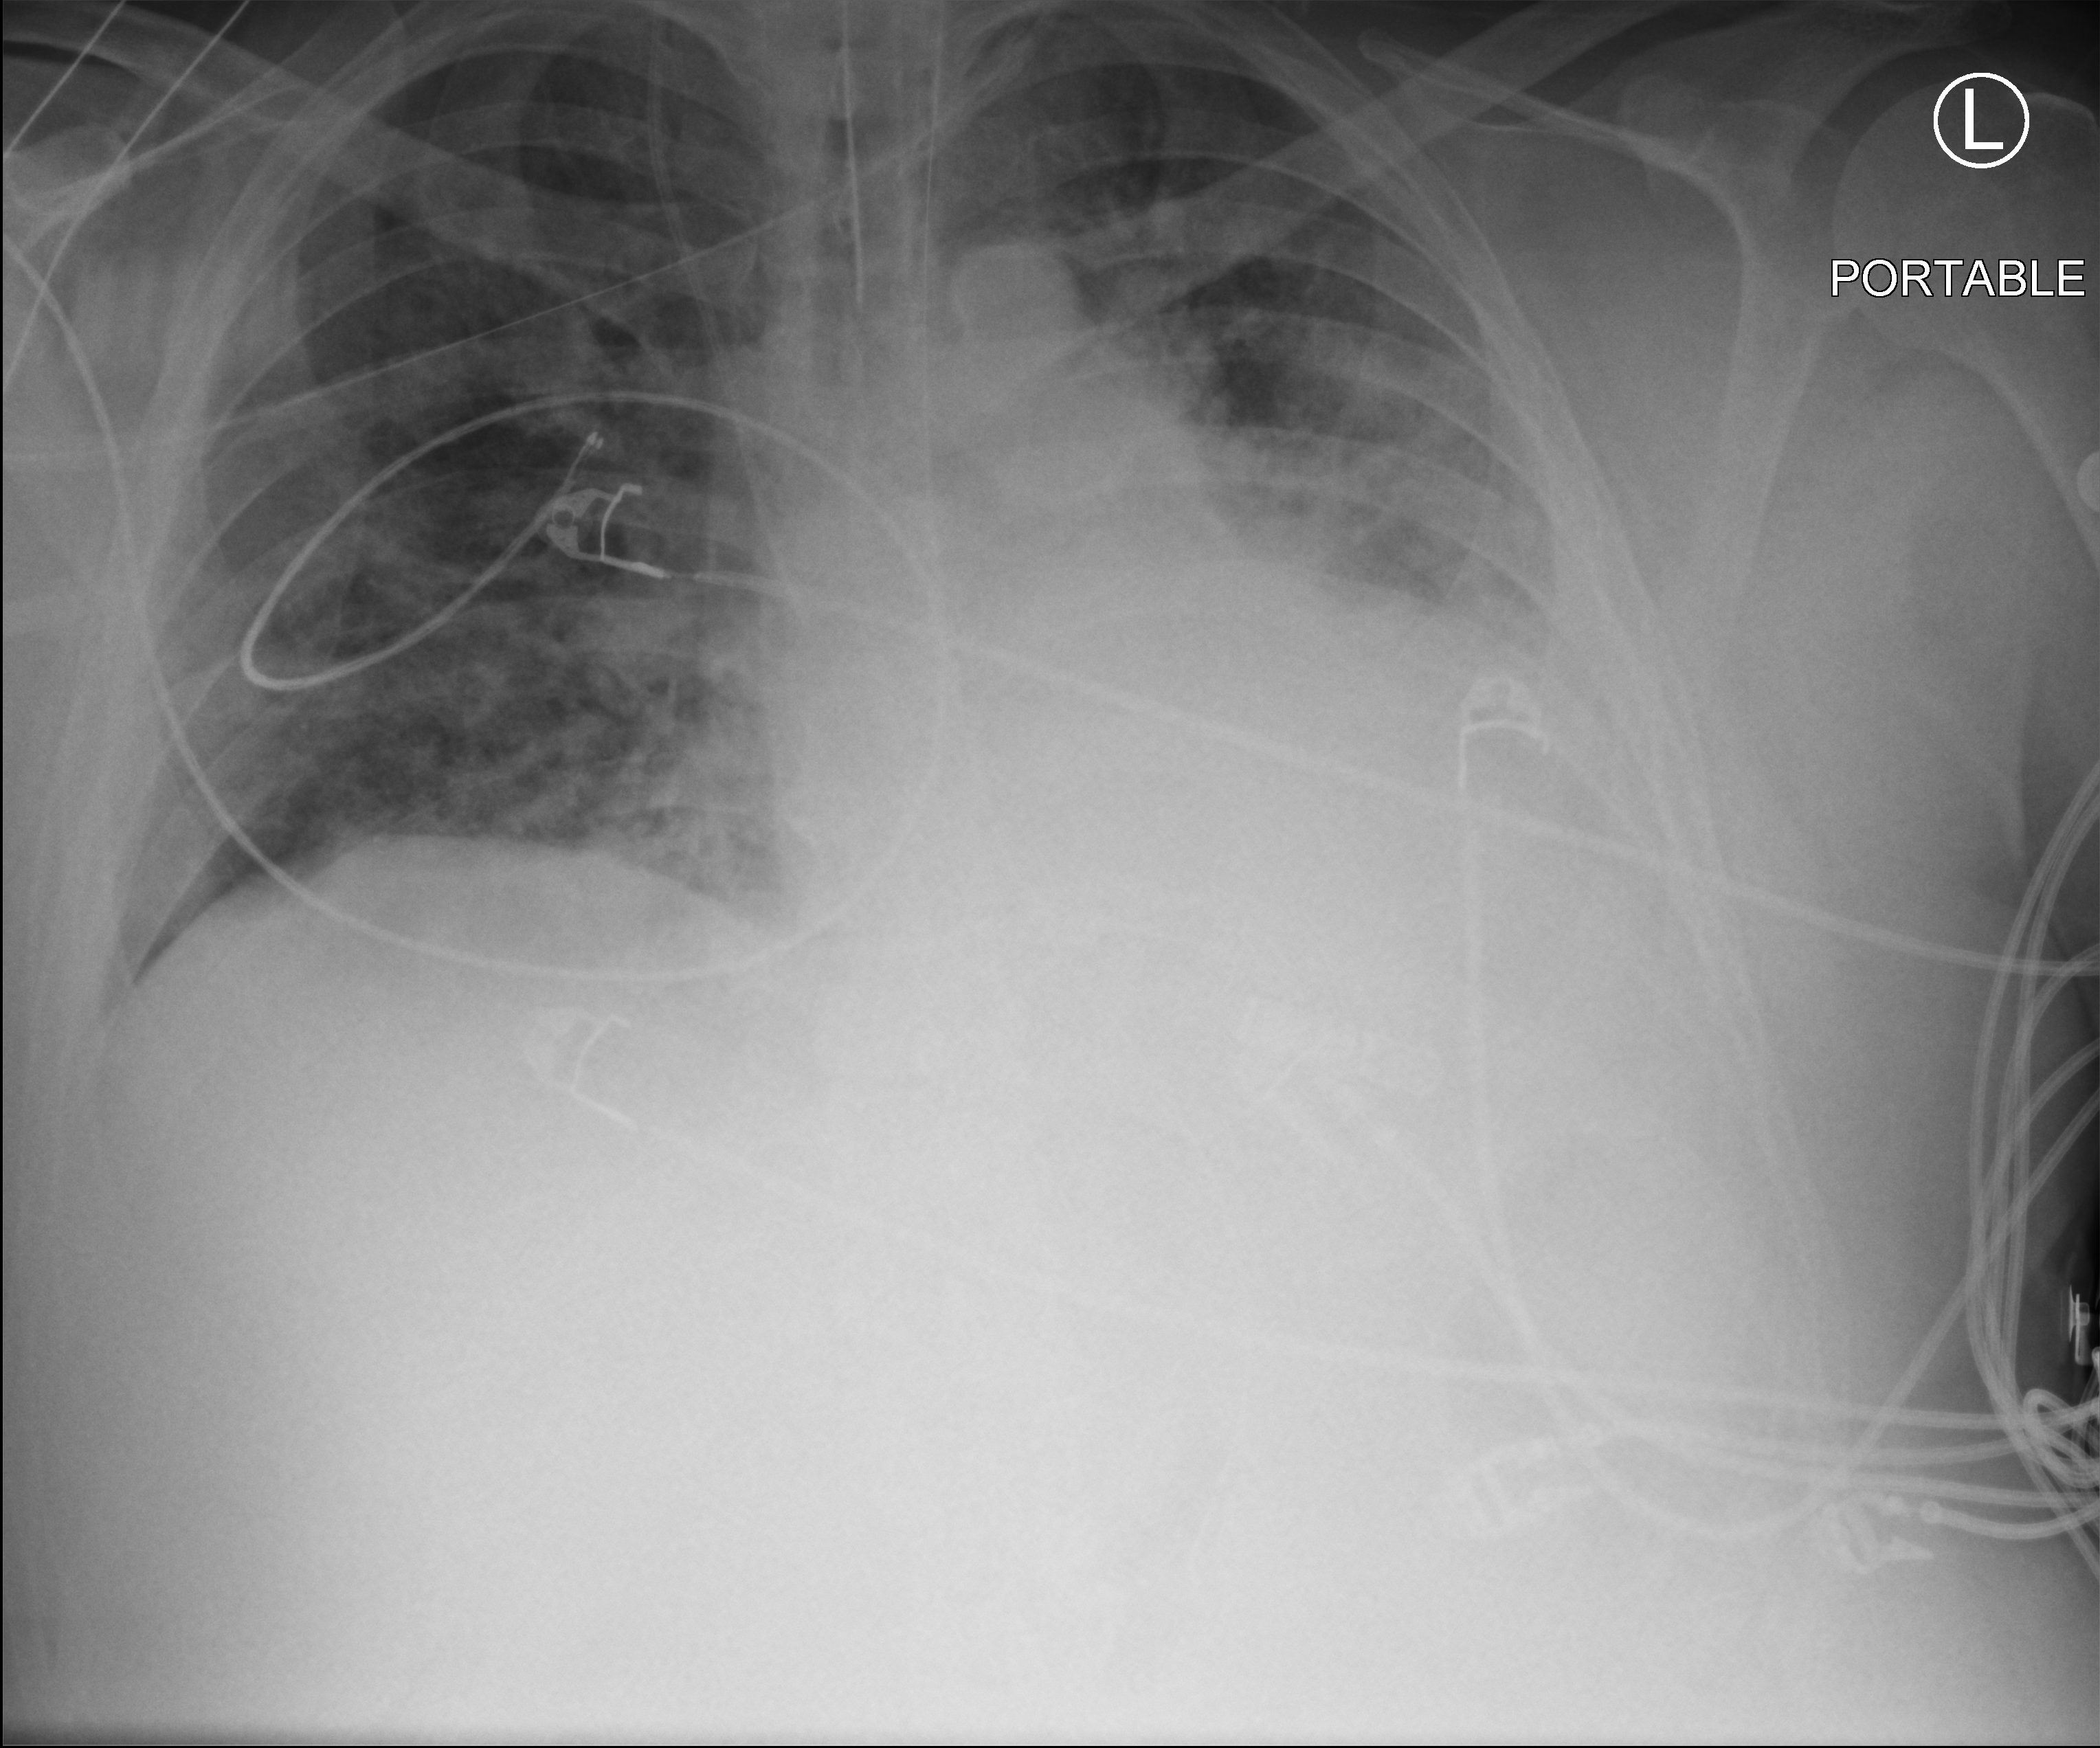
Bedside chest radiograph (computed radiography); anteroposterior (AP) projection. Male patient hospitalised with COVID-19, age 18–59 years.
Admission-level facts for this patient (not findings on this image; timing relative to this image not recorded): admitted to intensive care during this hospital stay: yes; length of hospital stay: 39 days; mechanically ventilated during this hospital stay: yes.